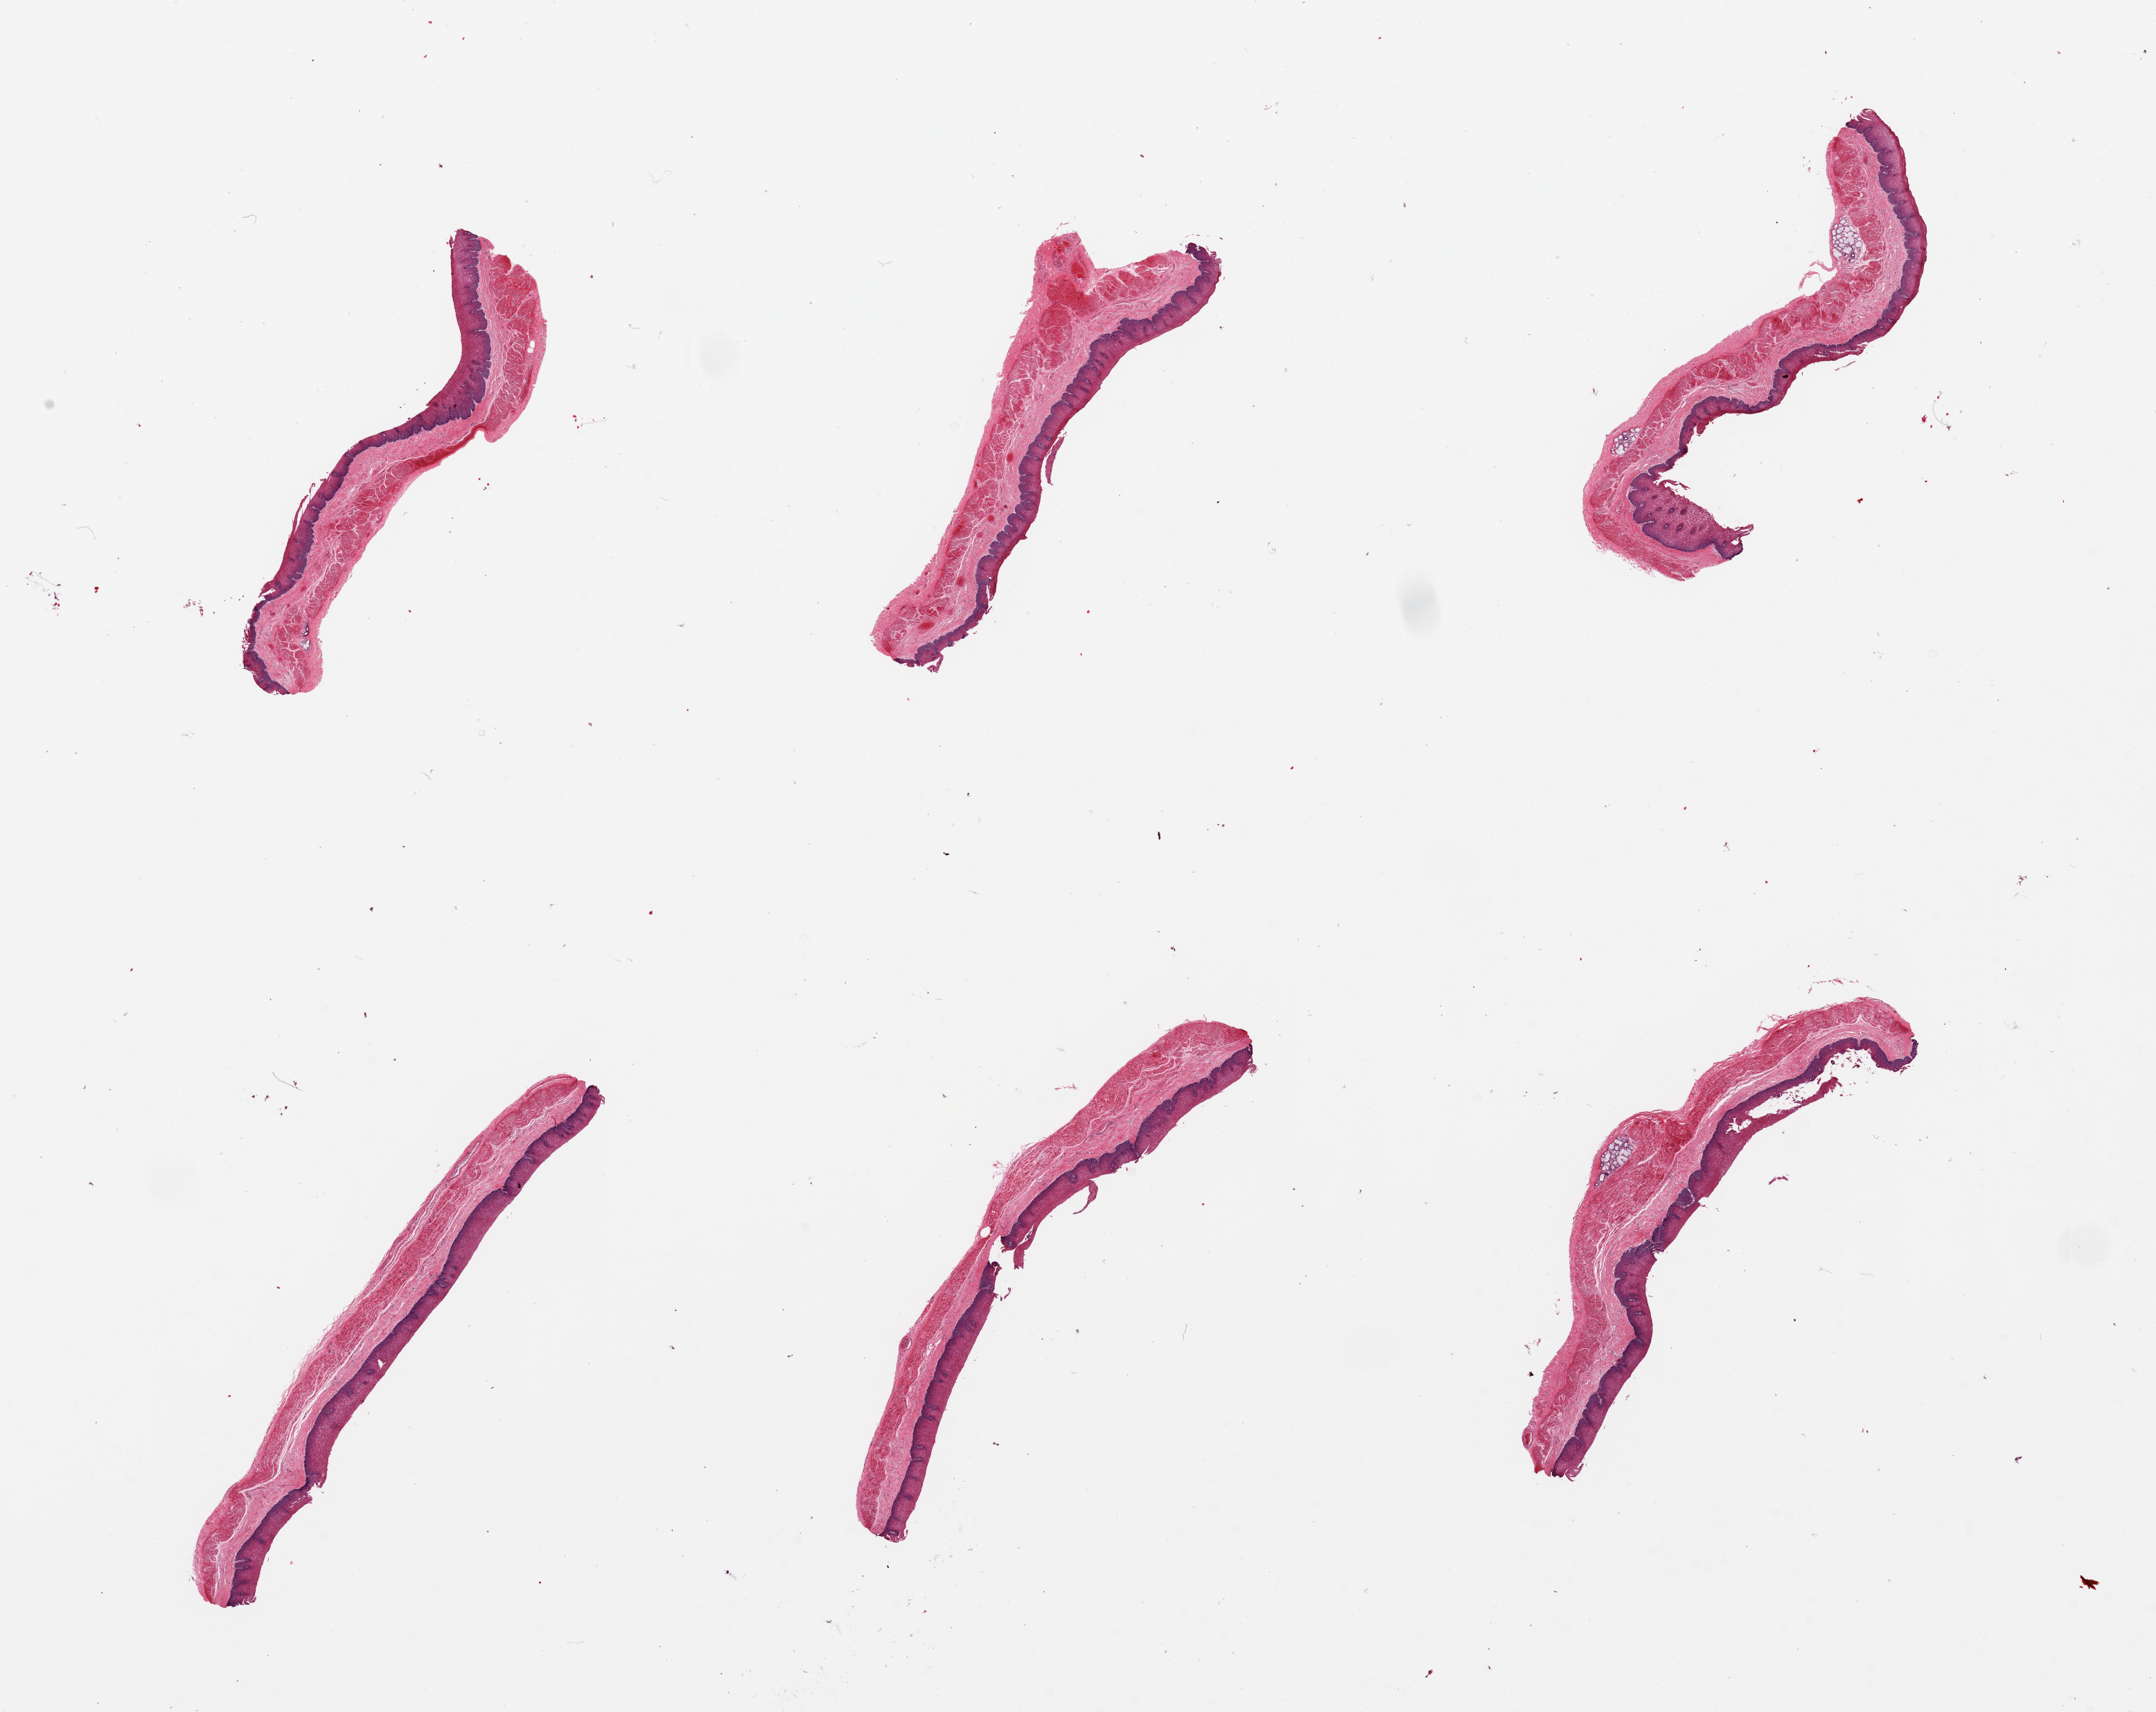
Digitized H&E-stained section, brightfield, whole scanned area (about 24.6 x 19.5 mm, slide scanned at 20x) shown as a low-resolution overview, PAXgene-fixed, paraffin-embedded tissue, section of esophageal mucous membrane (target tissue), tissue donor sample. Donor sex: female.
Reviewer comment on this tissue sample: 6 pieces, squamous mucosa is 20-30% of thickness, some foci of desquamation.